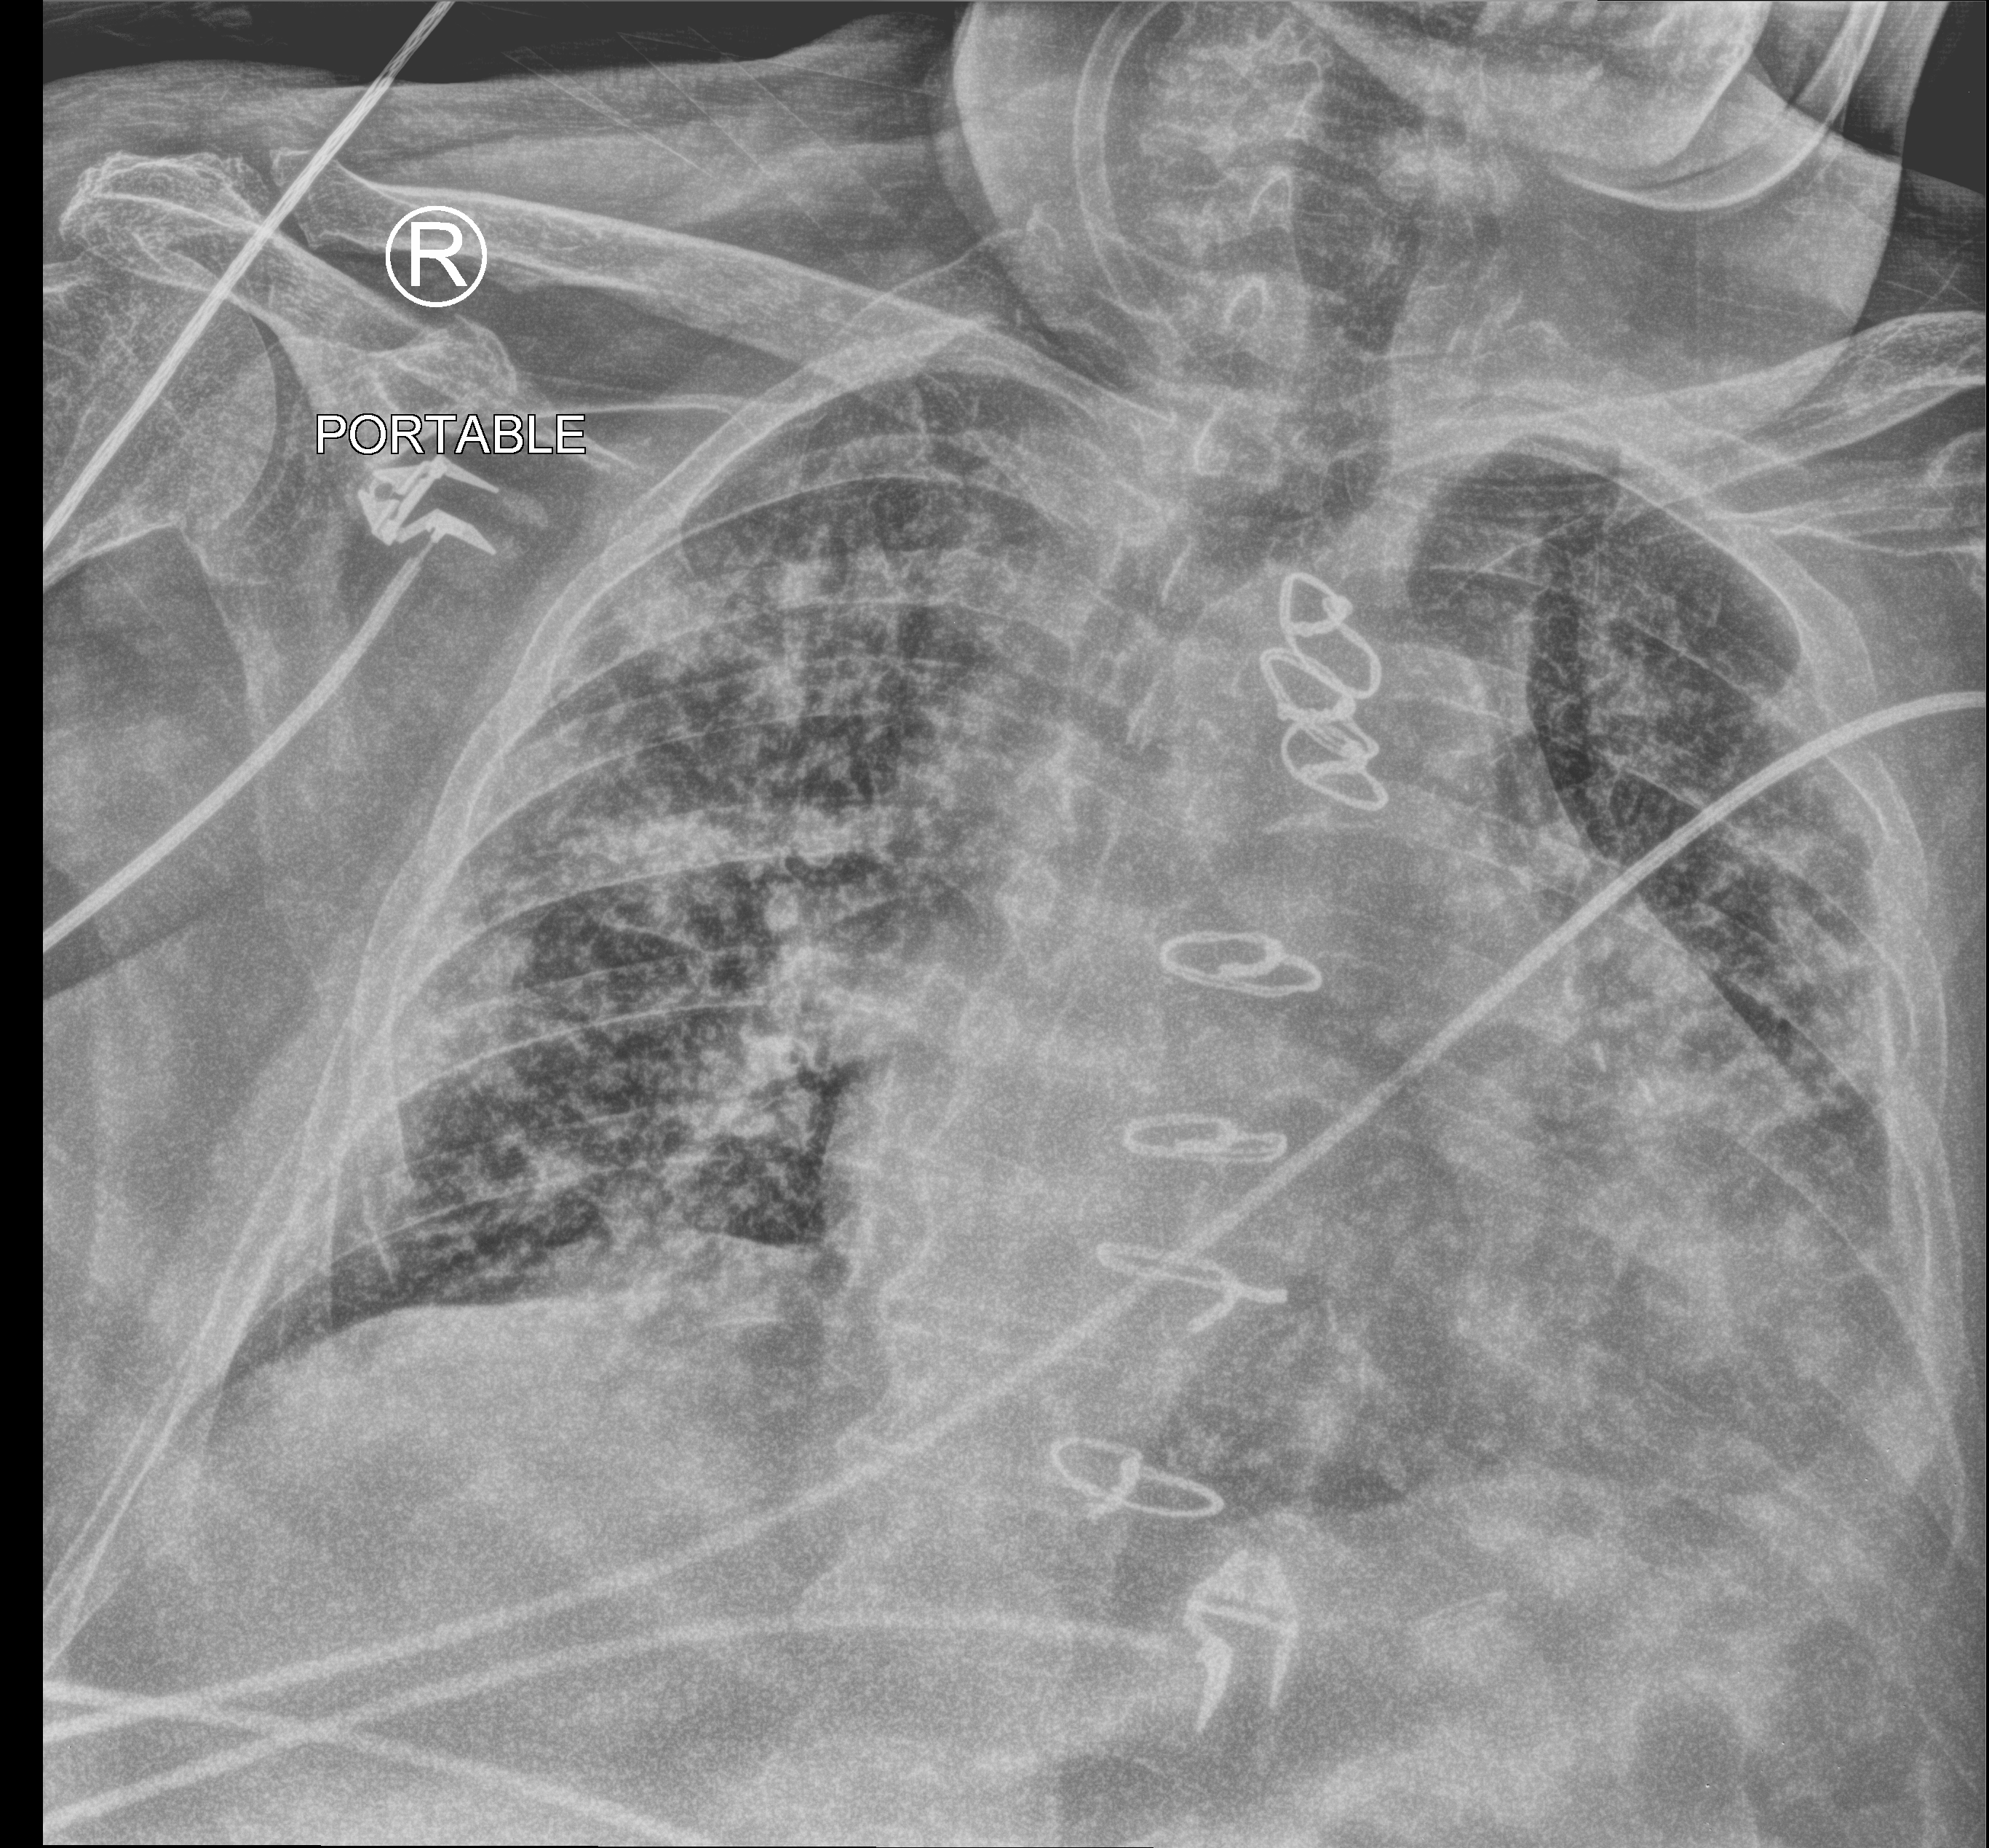
Chest X-ray (portable). Patient hospitalised with COVID-19; male, aged 75–90 years.
From the hospital-stay record, not from the radiograph (when in the stay this image was taken is not recorded): diabetes (admission record): no; mechanically ventilated during this hospital stay: no; length of hospital stay: 12 days.